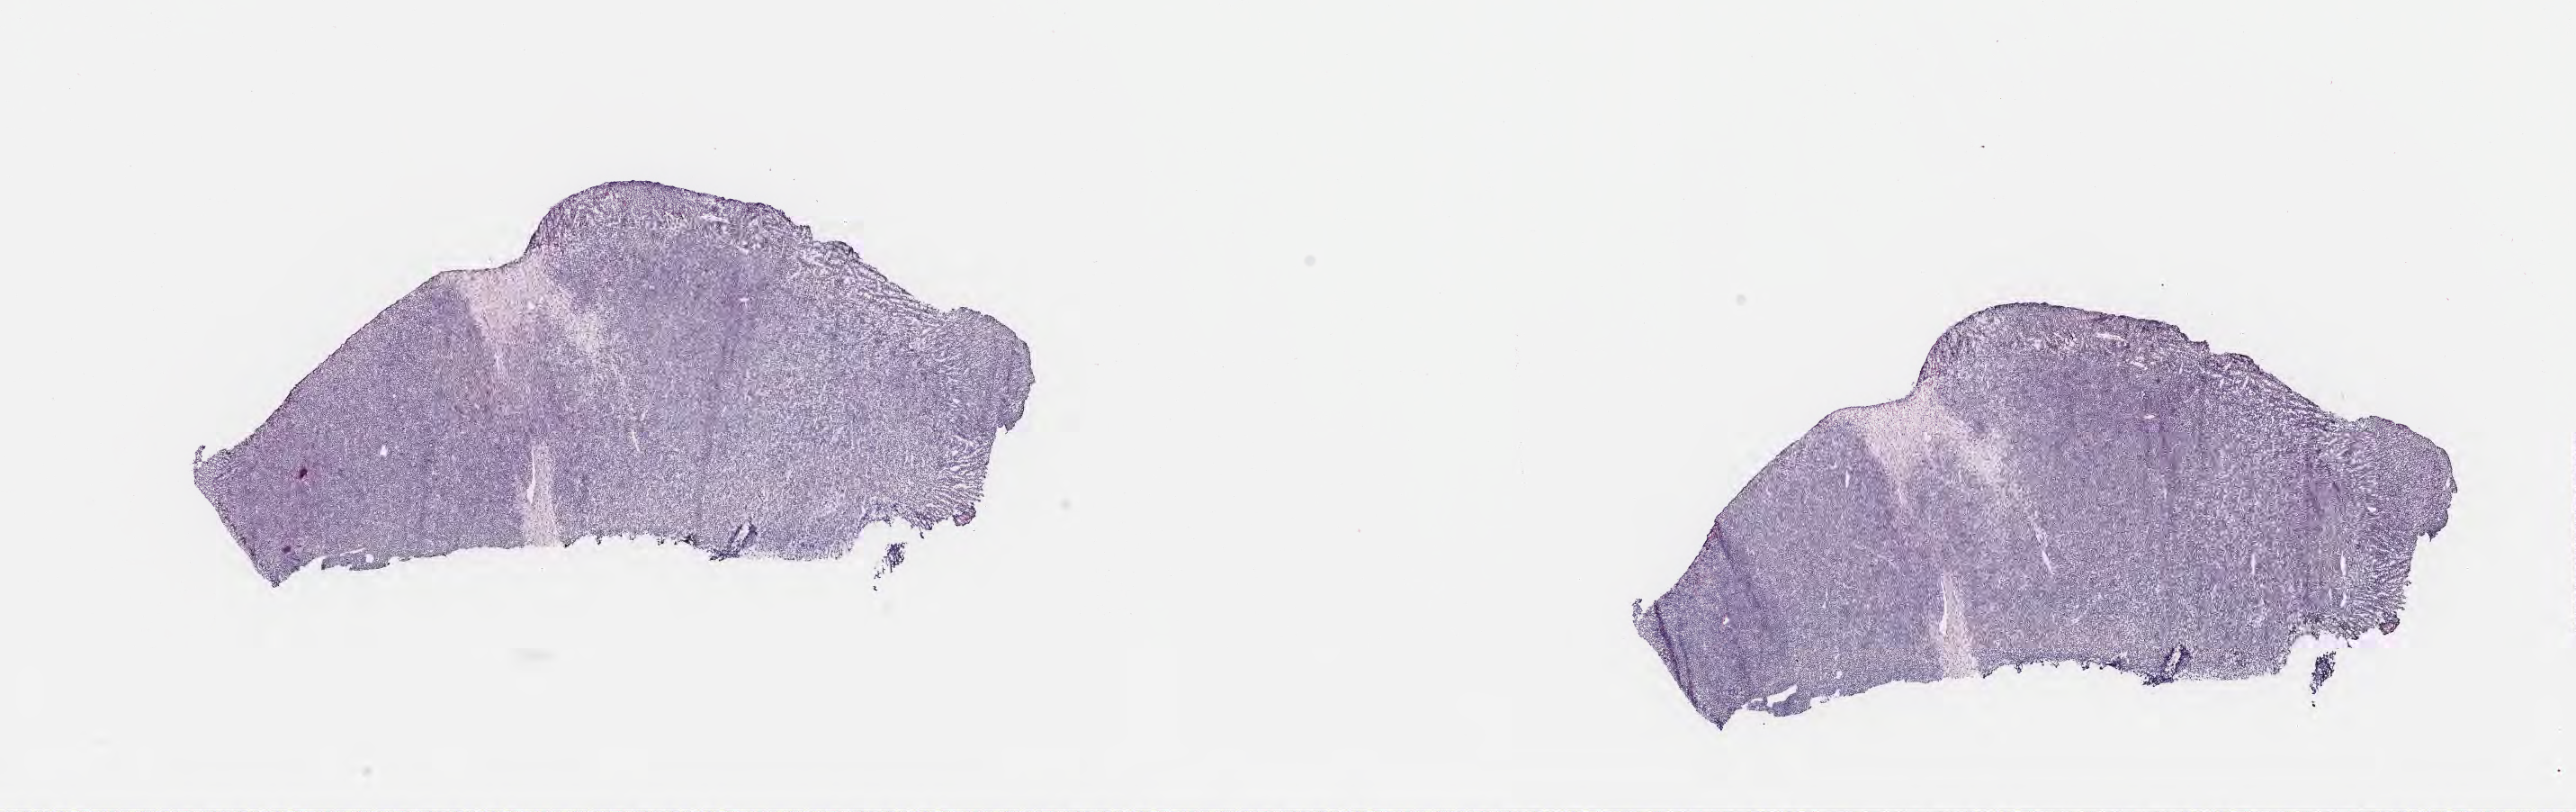
Digitized hematoxylin and eosin (H&E)-stained section — whole scanned area (about 23.1 x 7.3 mm) shown as a low-resolution overview; frozen section; primary tumor; anatomic site: cranium. Patient female; age 10 years. Composition of this section per pathologist review: tumor cells 80%, tumor nuclei 90%, stromal cells 15%, necrosis 5%, normal cells 0%. Inflammatory infiltration, as recorded: lymphocyte infiltration 80%, monocyte infiltration 10%, neutrophil infiltration 5%.
Diagnosis: Burkitt lymphoma, NOS. Section: top of the tissue portion. Ann Arbor stage (patient): Stage I.